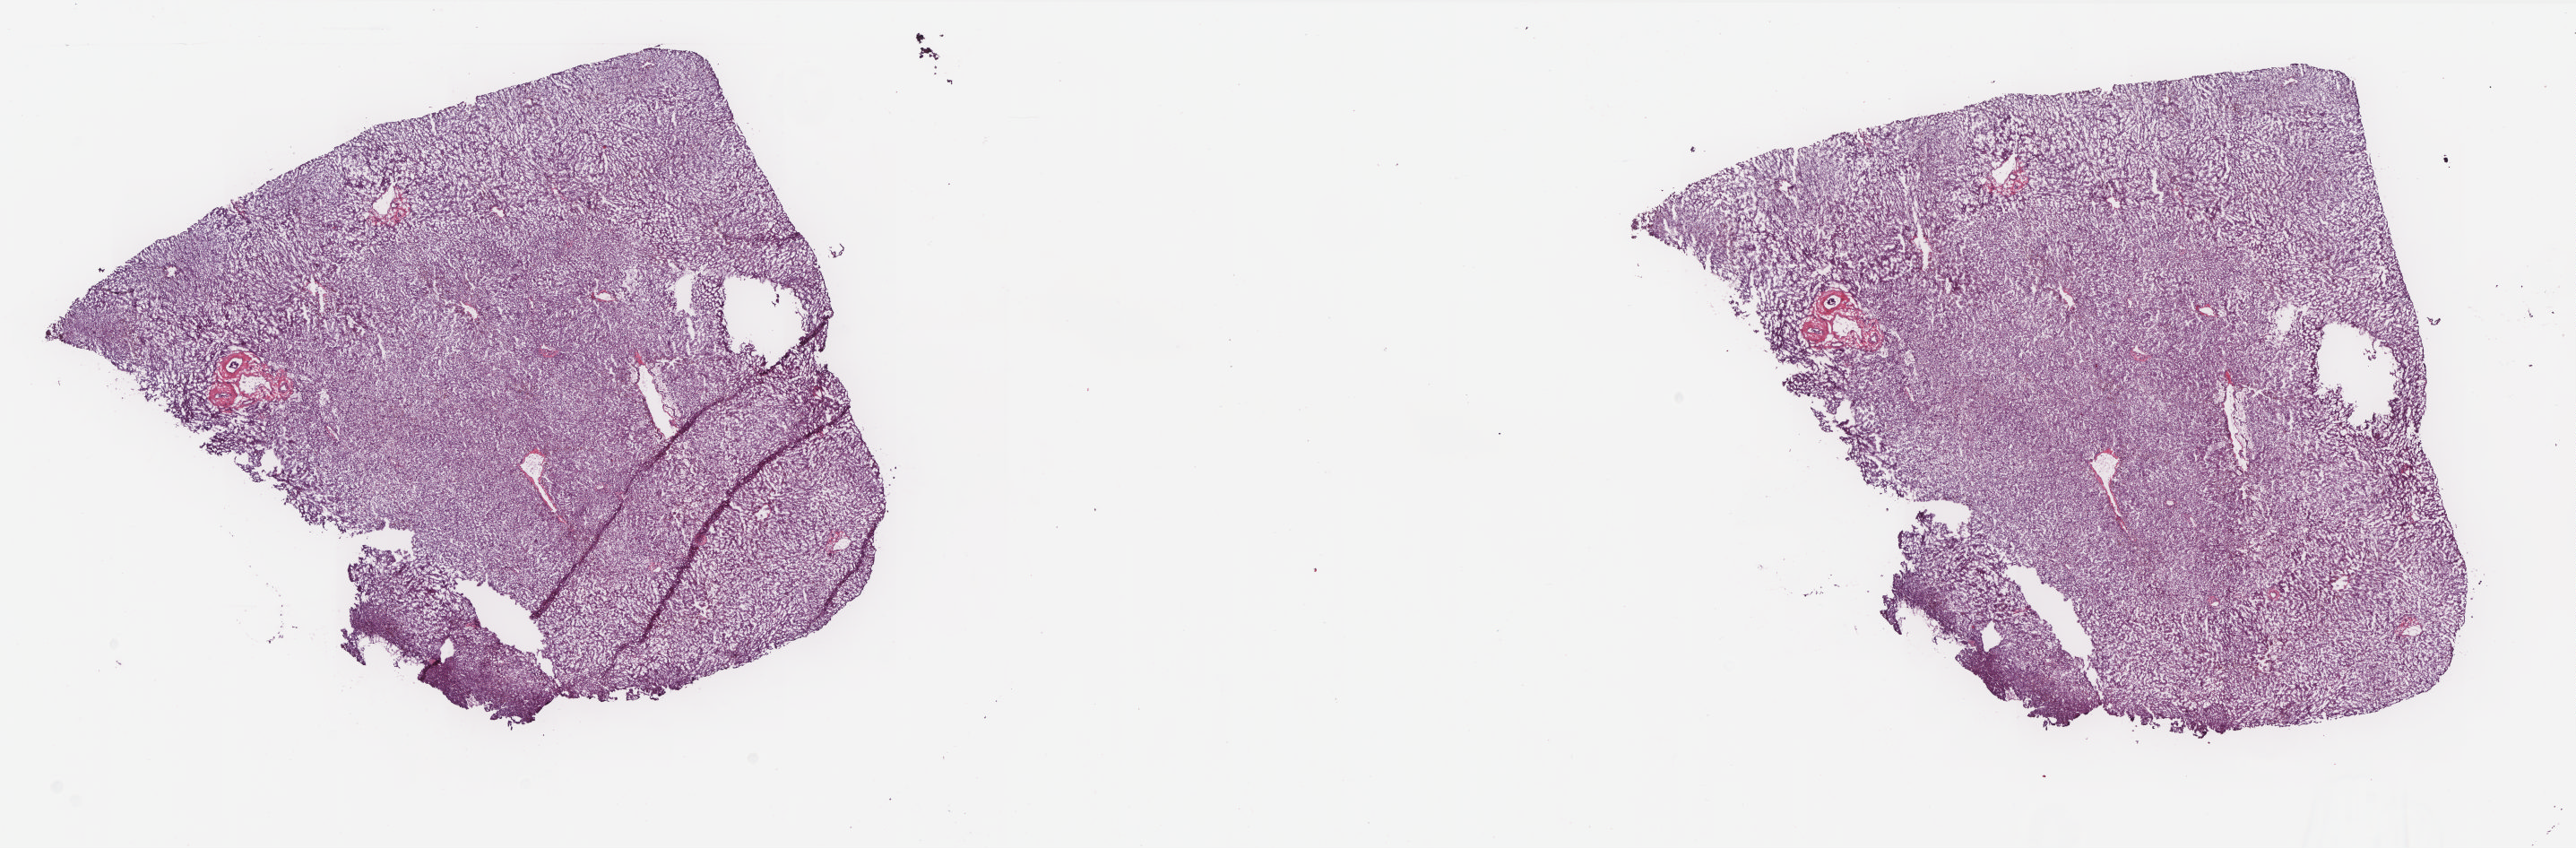
Whole-slide histology image, H&E-stained — low-resolution overview of the scanned area, about 23.0 x 7.6 mm (slide scanned at 20x); frozen section from the top of the tissue portion; liver, solid tissue normal (non-tumour tissue) sample. Female patient; age at initial diagnosis 64 years. Slide review estimates, as recorded: tumour cells 0%, tumour nuclei 0%, normal cells 70%, stromal cells 30%, necrosis 0%. Inflammatory infiltration, as recorded: lymphocyte infiltration 0%, monocyte infiltration 0%, neutrophil infiltration 0%.
• this section: solid tissue normal (non-tumour) sample from the same patient
• patient diagnosis: Hepatocellular carcinoma, NOS